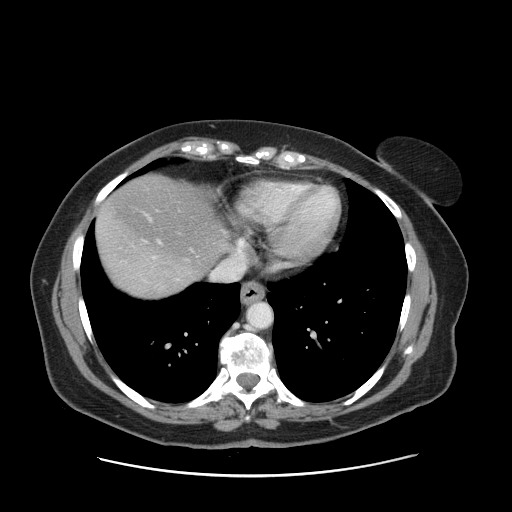
Contrast-enhanced abdominal CT, one axial slice. 120 kVp. Intravenous contrast given. Soft-tissue window (W 400 / L 40 HU). 2.5 mm slice thickness. 512 × 512 image matrix, field of view 398 × 398 mm. Female patient, age 62 years. From the clinical record (not read from this slice): diagnosis: colorectal cancer liver metastases, imaged before liver resection; multiple liver metastases: no; largest metastasis: 2.5 cm; disease in both lobes: no.
Outlined on this slice (outlined manually by an expert reader):
- hepatic veins: bounding box <144,241,162,258> (left, top, right, bottom; pixels)
- liver: <97,175,223,299>
- planned liver remnant (the part of the liver to remain after resection): <98,175,223,274>